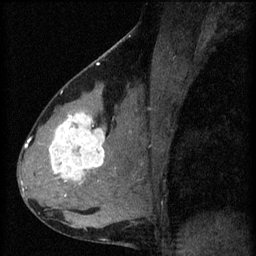
Breast MRI (dynamic contrast-enhanced), one sagittal slice. Slice 34 of 60 in the series (ordered by position). 3 images stored at this slice position (order not interpretable as contrast timing). 1.5 T. TE 4.2 ms, TR 8.2 ms. 2 mm slice thickness. 256 × 256 image matrix, field of view 180 × 180 mm. Female patient, age 37 years.
Structures marked on this image (semi-automatic segmentation, software-assisted and operator-edited):
- analysis volume of interest (the breast-tissue region the enhancement analysis was run in; not a lesion): bounding box [x1, y1, x2, y2] px = [44, 100, 119, 197]
- tumour enhancement mask (voxels above the 70 % enhancement threshold inside the analysis volume of interest): [50, 112, 106, 185]